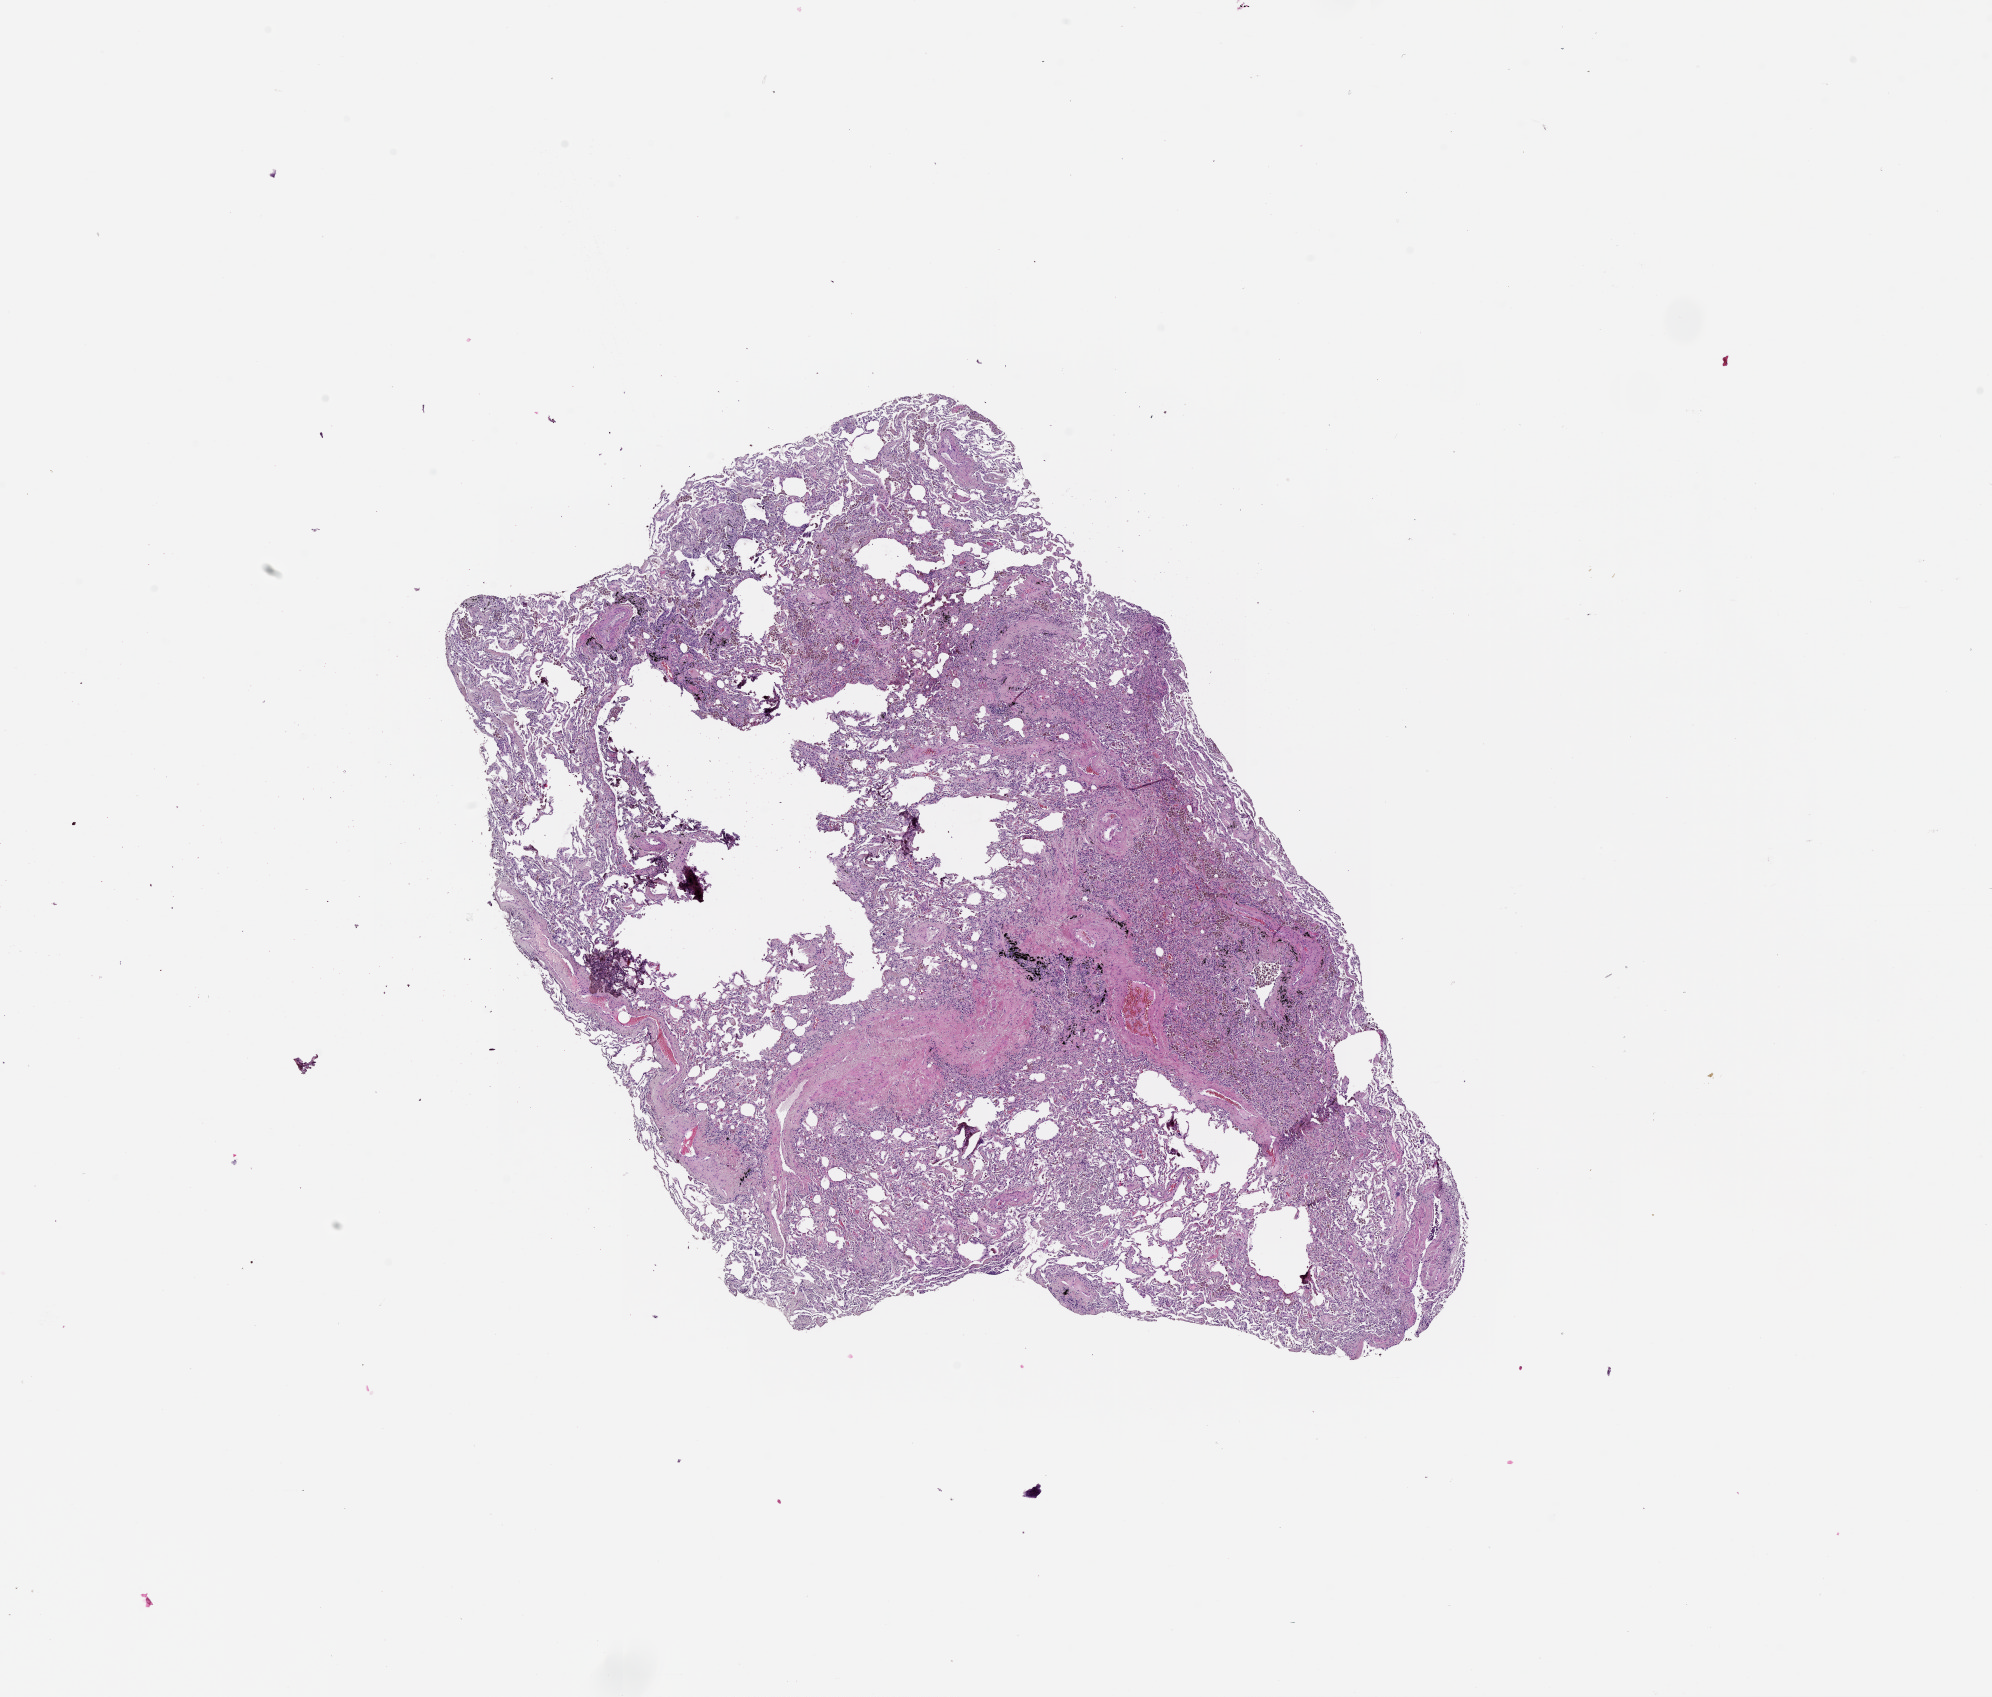
Digitized H&E tissue section (whole slide), whole scanned area (about 16.0 x 13.7 mm, slide scanned at 20x) shown as a low-resolution overview, normal (non-tumour) tissue sample, lung. Patient: male, age 54 years.
This section: normal (non-tumour) tissue from the same patient. Patient diagnosis (cohort enrolment): squamous cell carcinoma (lung).